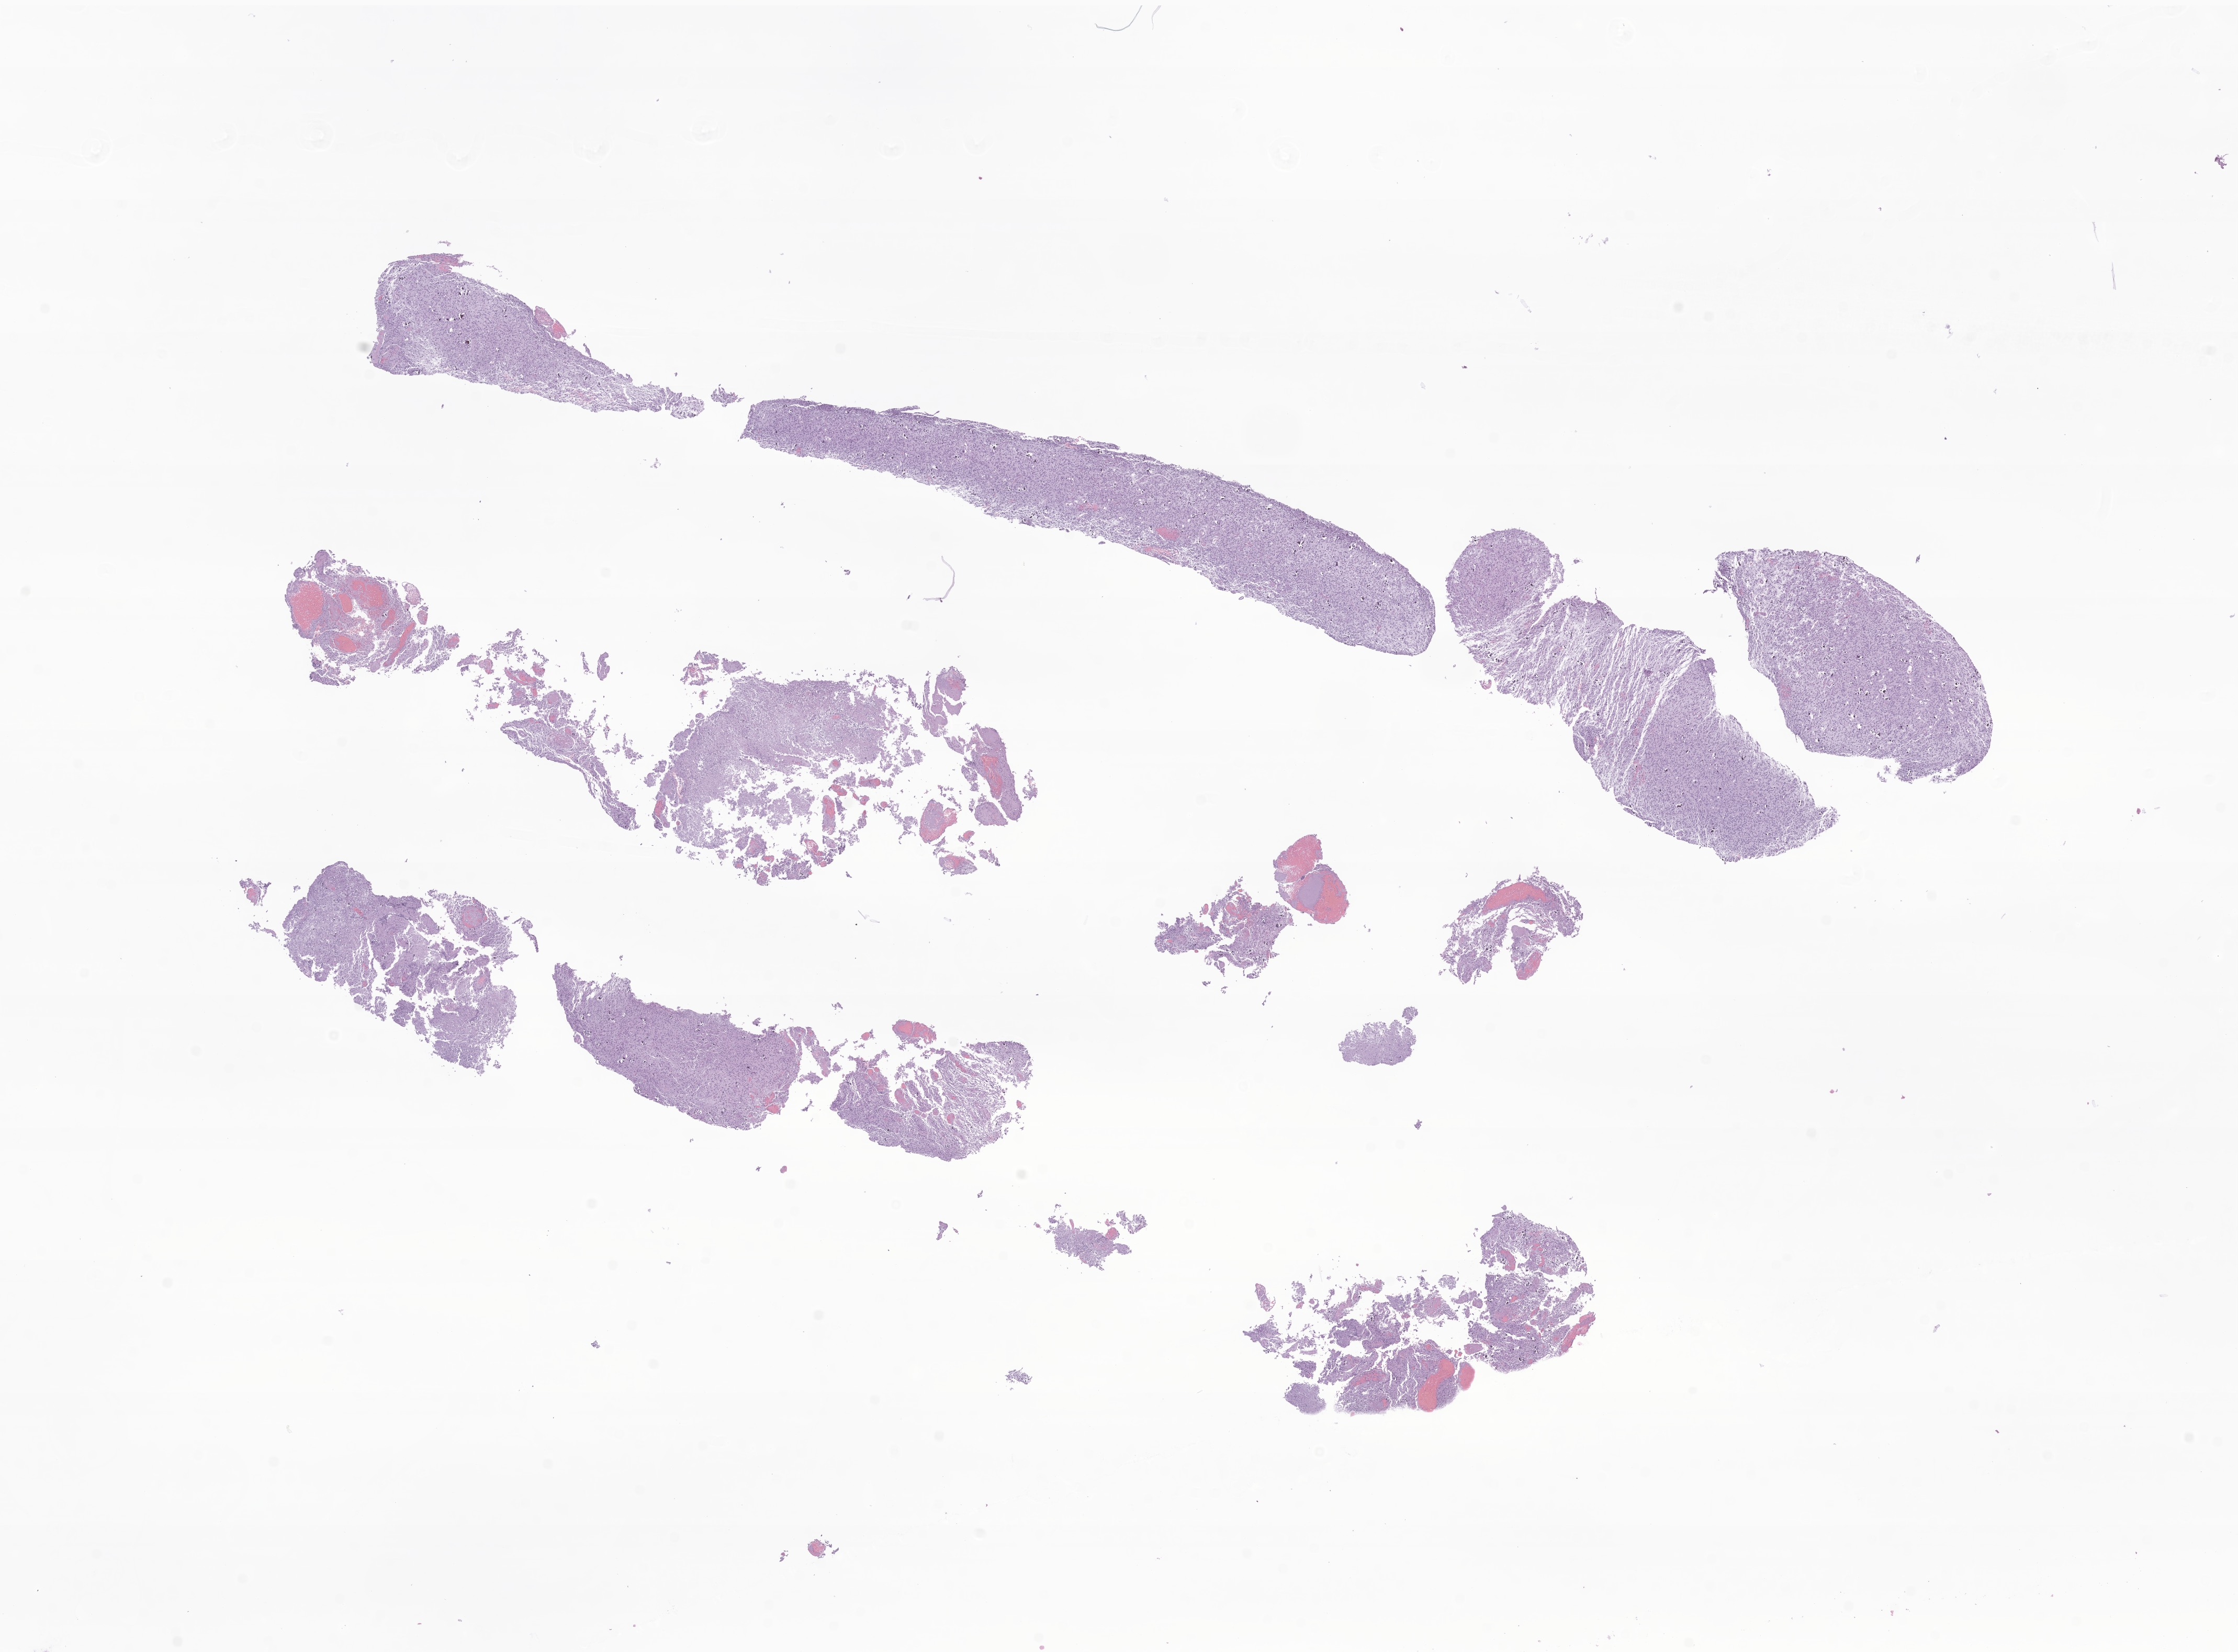
Digitized hematoxylin and eosin (H&E)-stained section of tumor tissue from the brain — shown as a low-resolution overview of the whole scanned area (about 18.0 x 13.3 mm). Formalin-fixed, paraffin-embedded (FFPE) tissue. Male patient, age 122 months (10 years 2 months).
Diagnosis: Glioma, malignant.